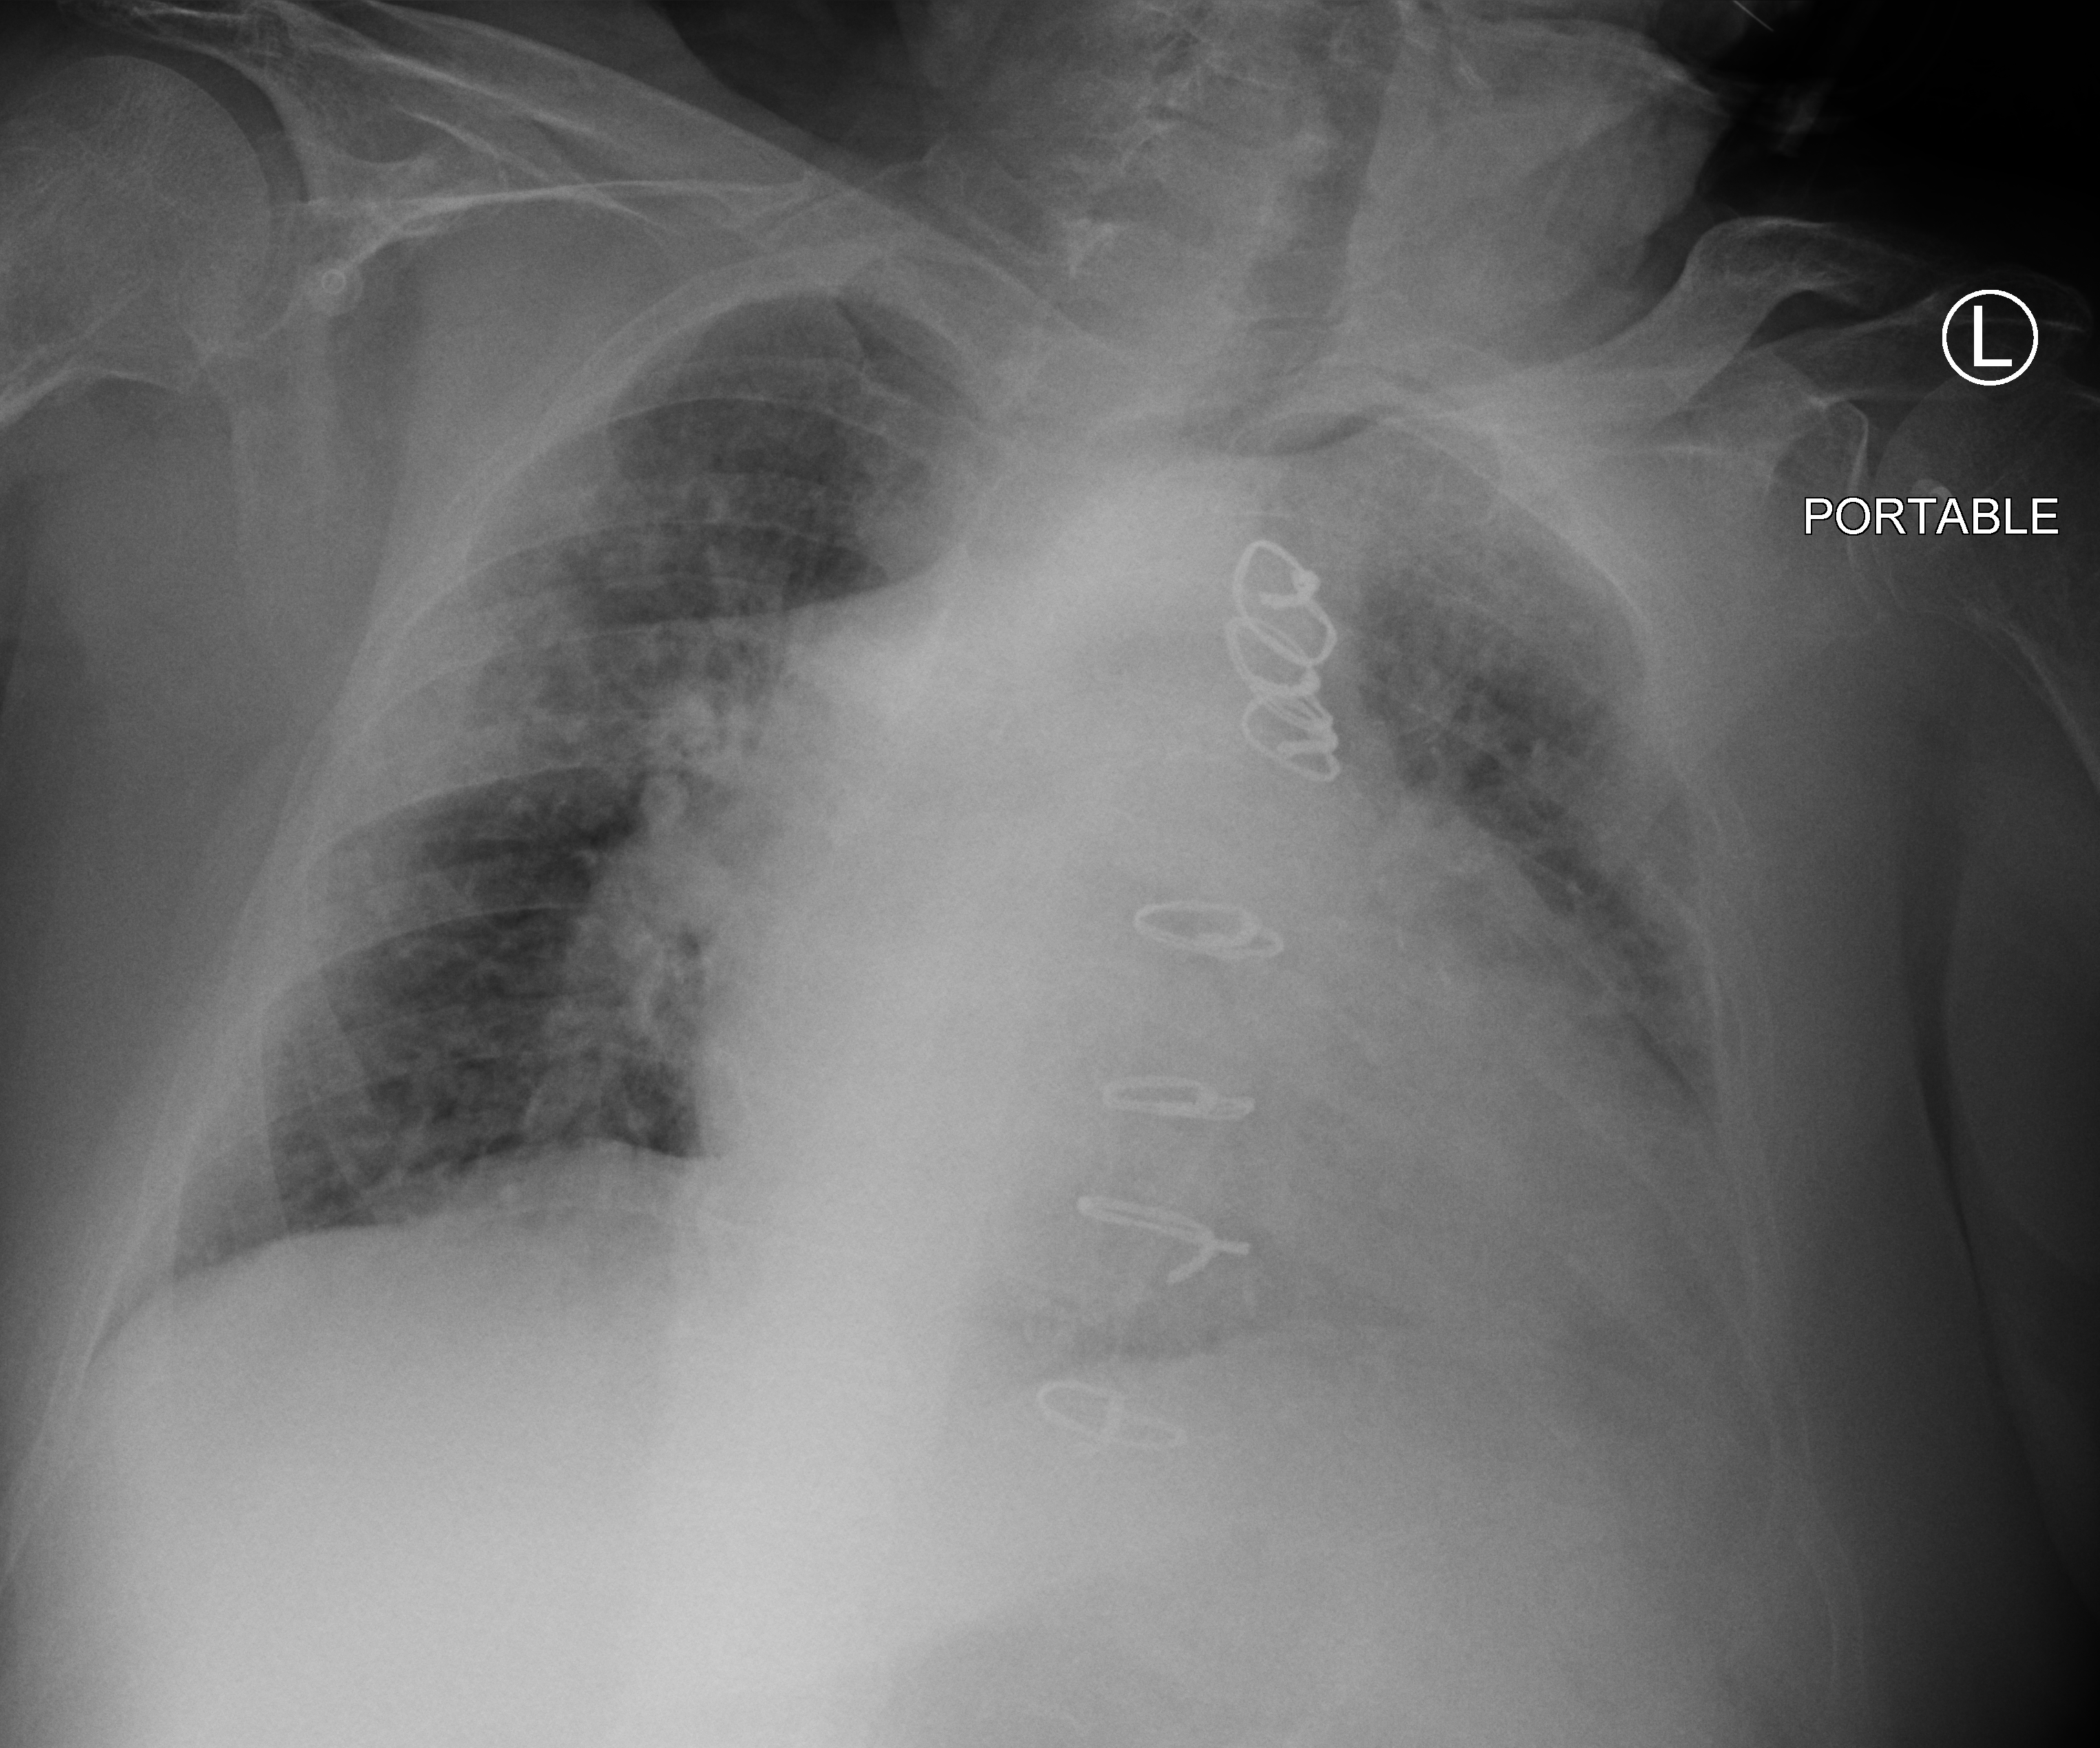
Portable chest radiograph; anteroposterior (AP) projection. Patient hospitalised with COVID-19; male, aged 75–90 years.
From the hospital-stay record, not from the radiograph (when in the stay this image was taken is not recorded):
- chronic kidney disease (admission record): no